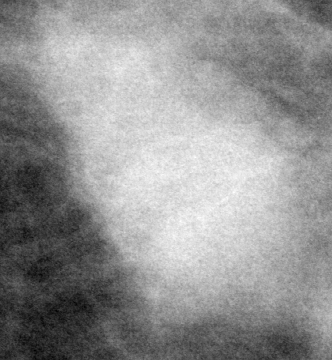
Region of interest cut from a scanned film mammogram (one marked finding); left breast; CC view.
Finding: mass, margins ill defined; BI-RADS assessment category 5; pathology (as recorded): malignant.